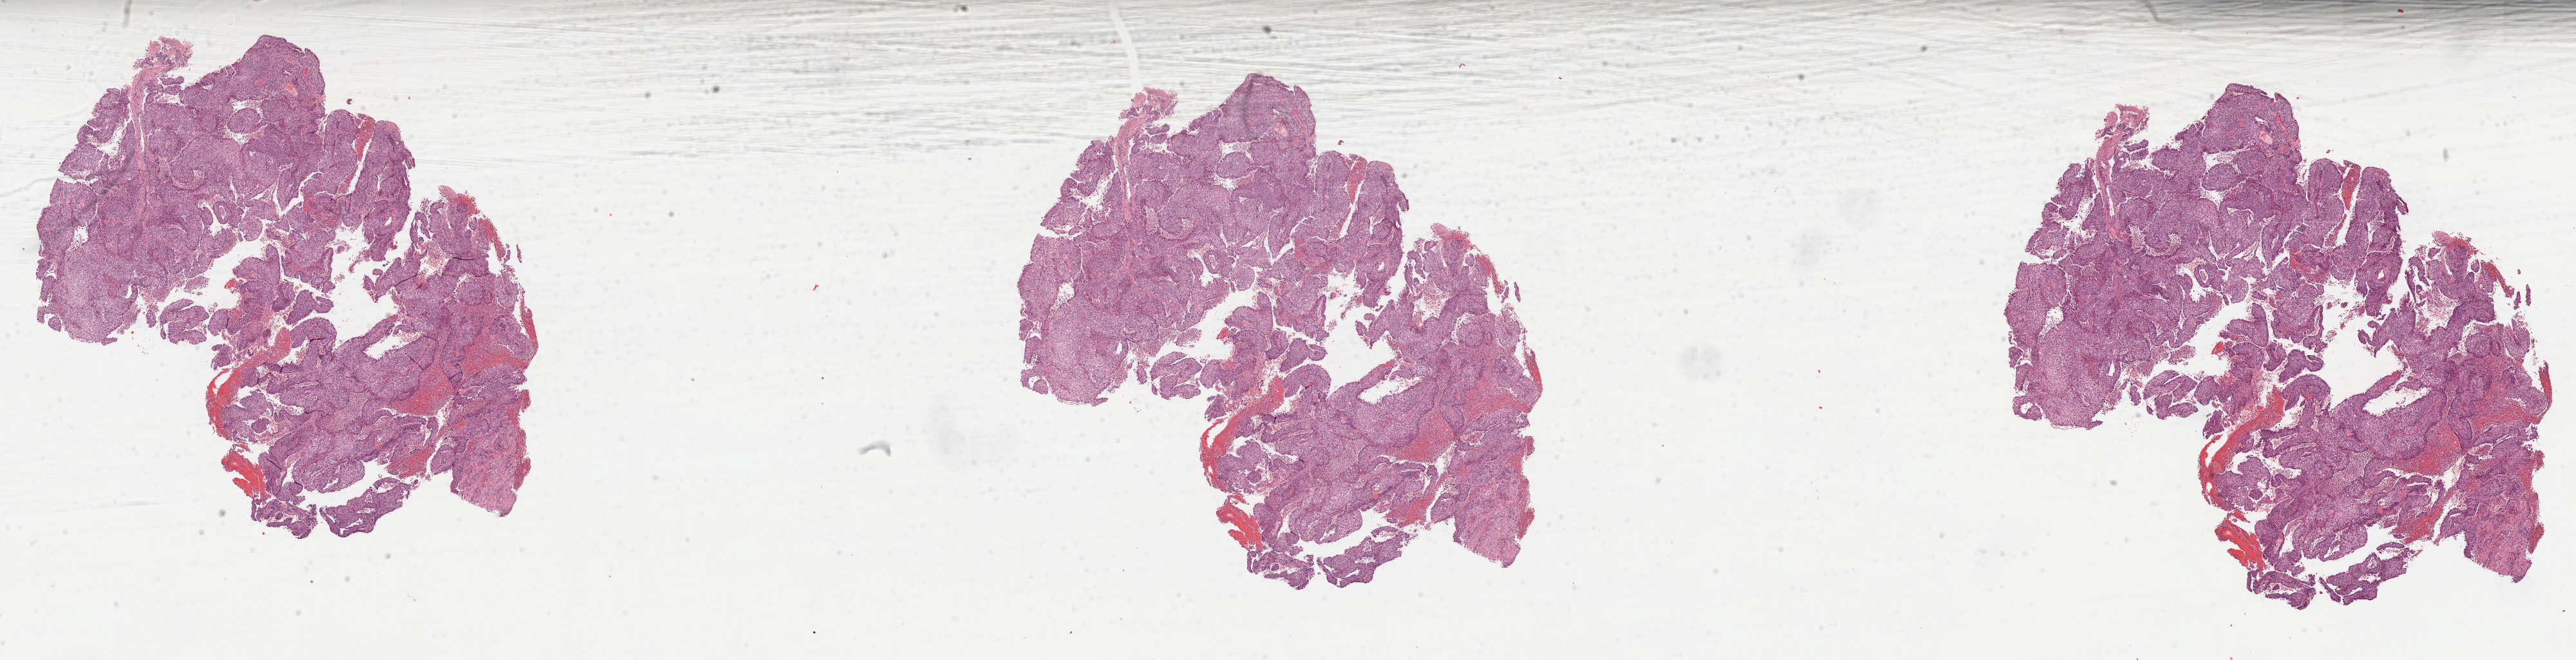
Whole-slide histology image, H&E, a low-resolution overview of the entire scanned area, about 32.0 x 8.2 mm, formalin-fixed paraffin-embedded (FFPE) diagnostic section, primary tumour sample from the lung. Male patient; age at initial diagnosis 63 years.
AJCC pathologic stage: IA. Histologic diagnosis: Squamous cell carcinoma, NOS (lower lobe, lung).